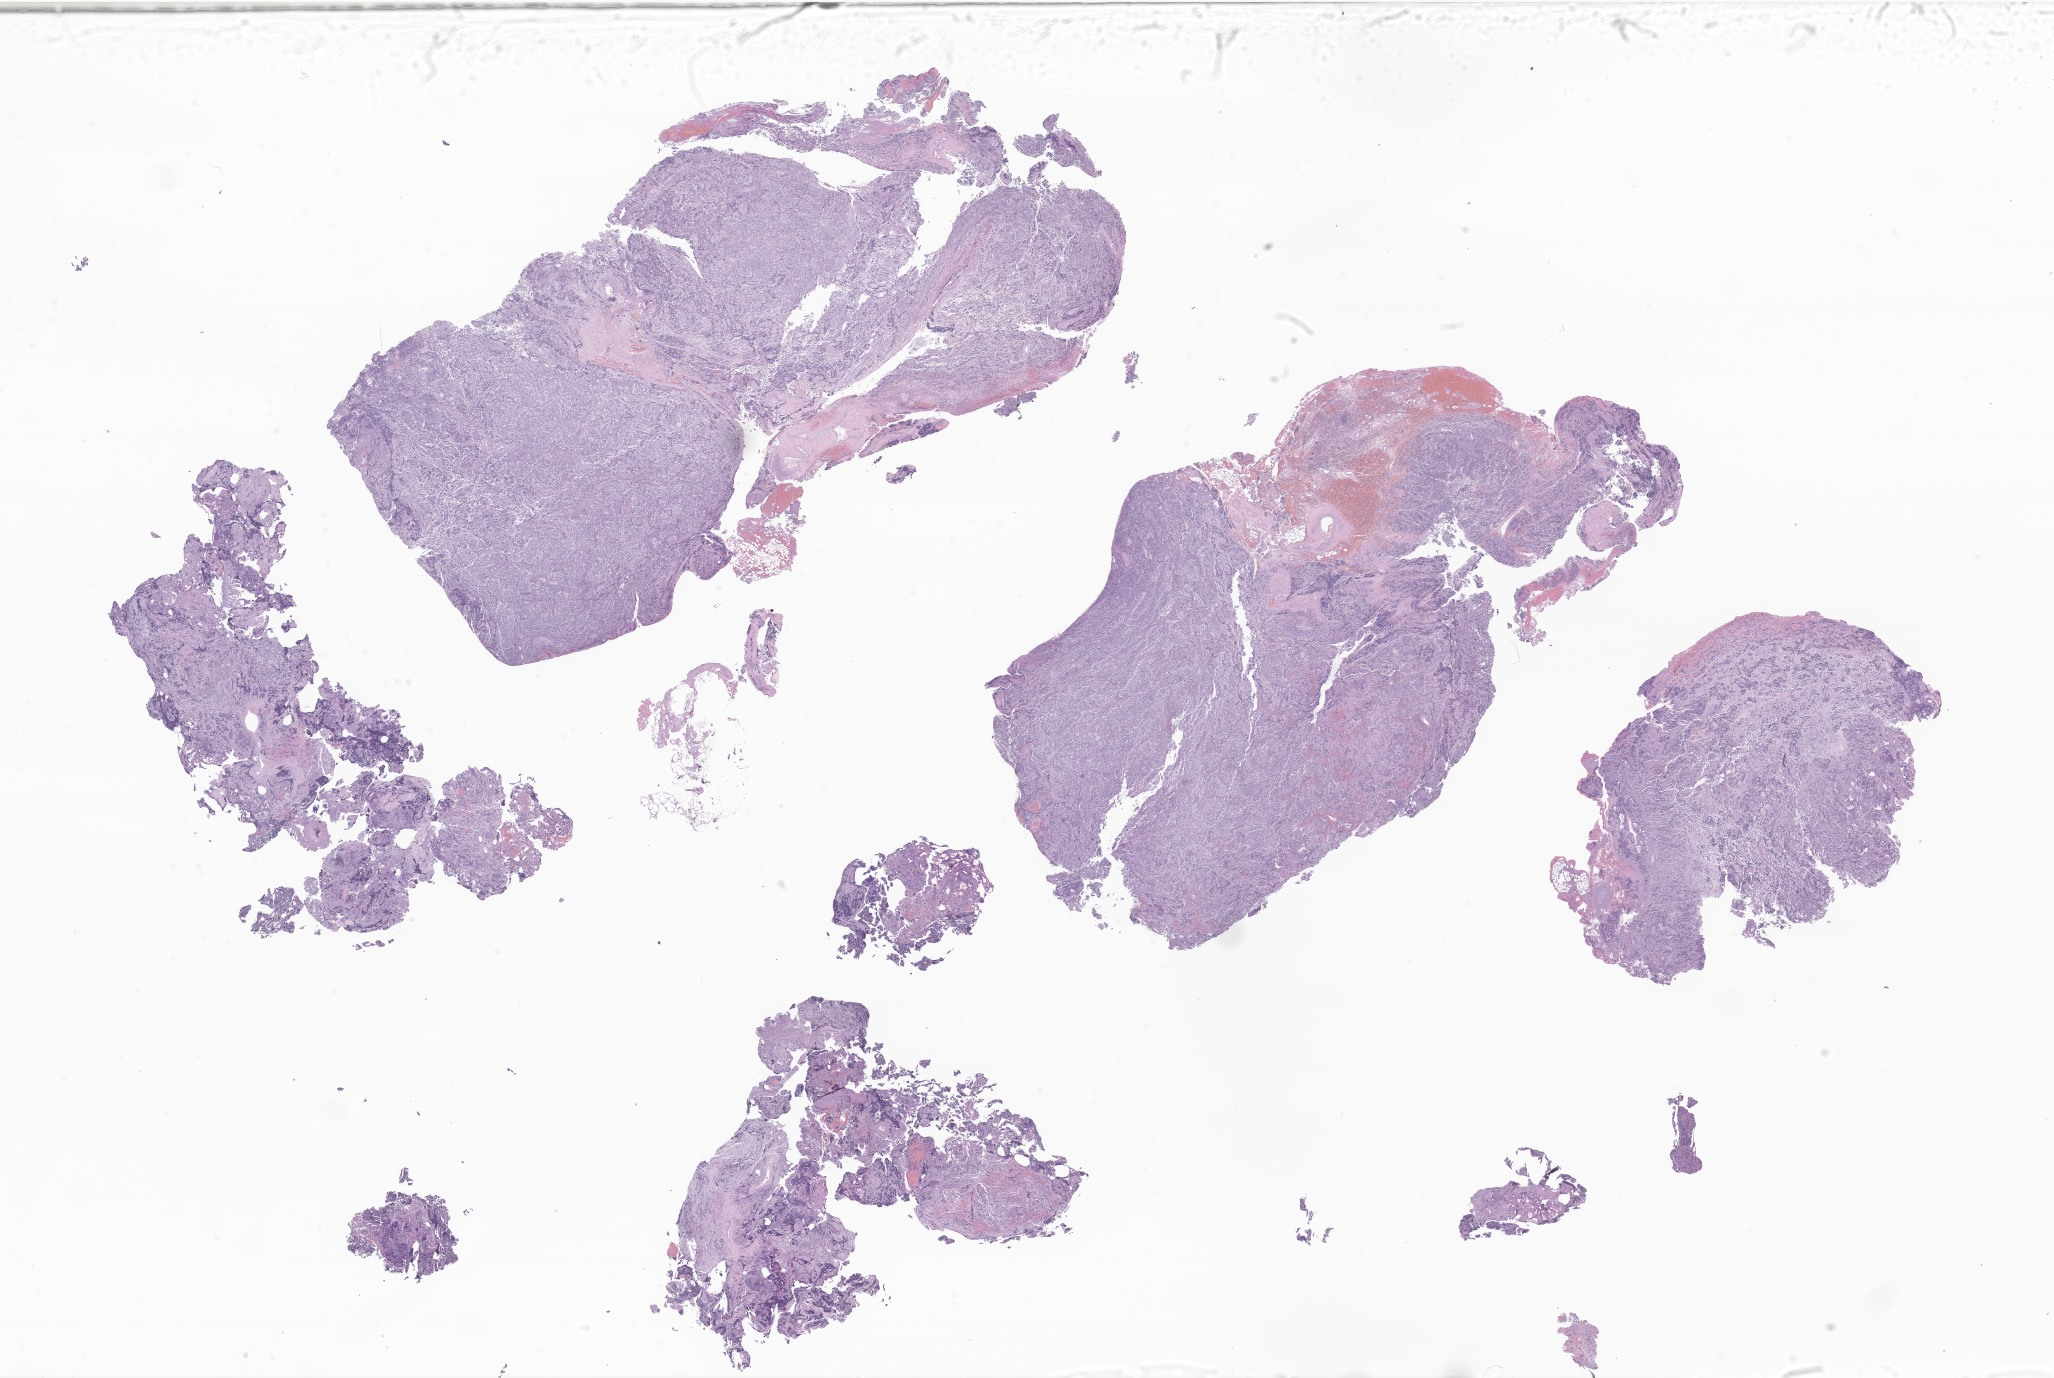
Digitized haematoxylin and eosin-stained section of tumor tissue from the retroperitoneum — shown as a low-resolution overview of the whole scanned area (about 34.6 x 23.2 mm). Formalin-fixed paraffin-embedded section. Patient: female, age 43 days.
Diagnosis (ICD-O-3 morphology term): Neuroblastoma, NOS.